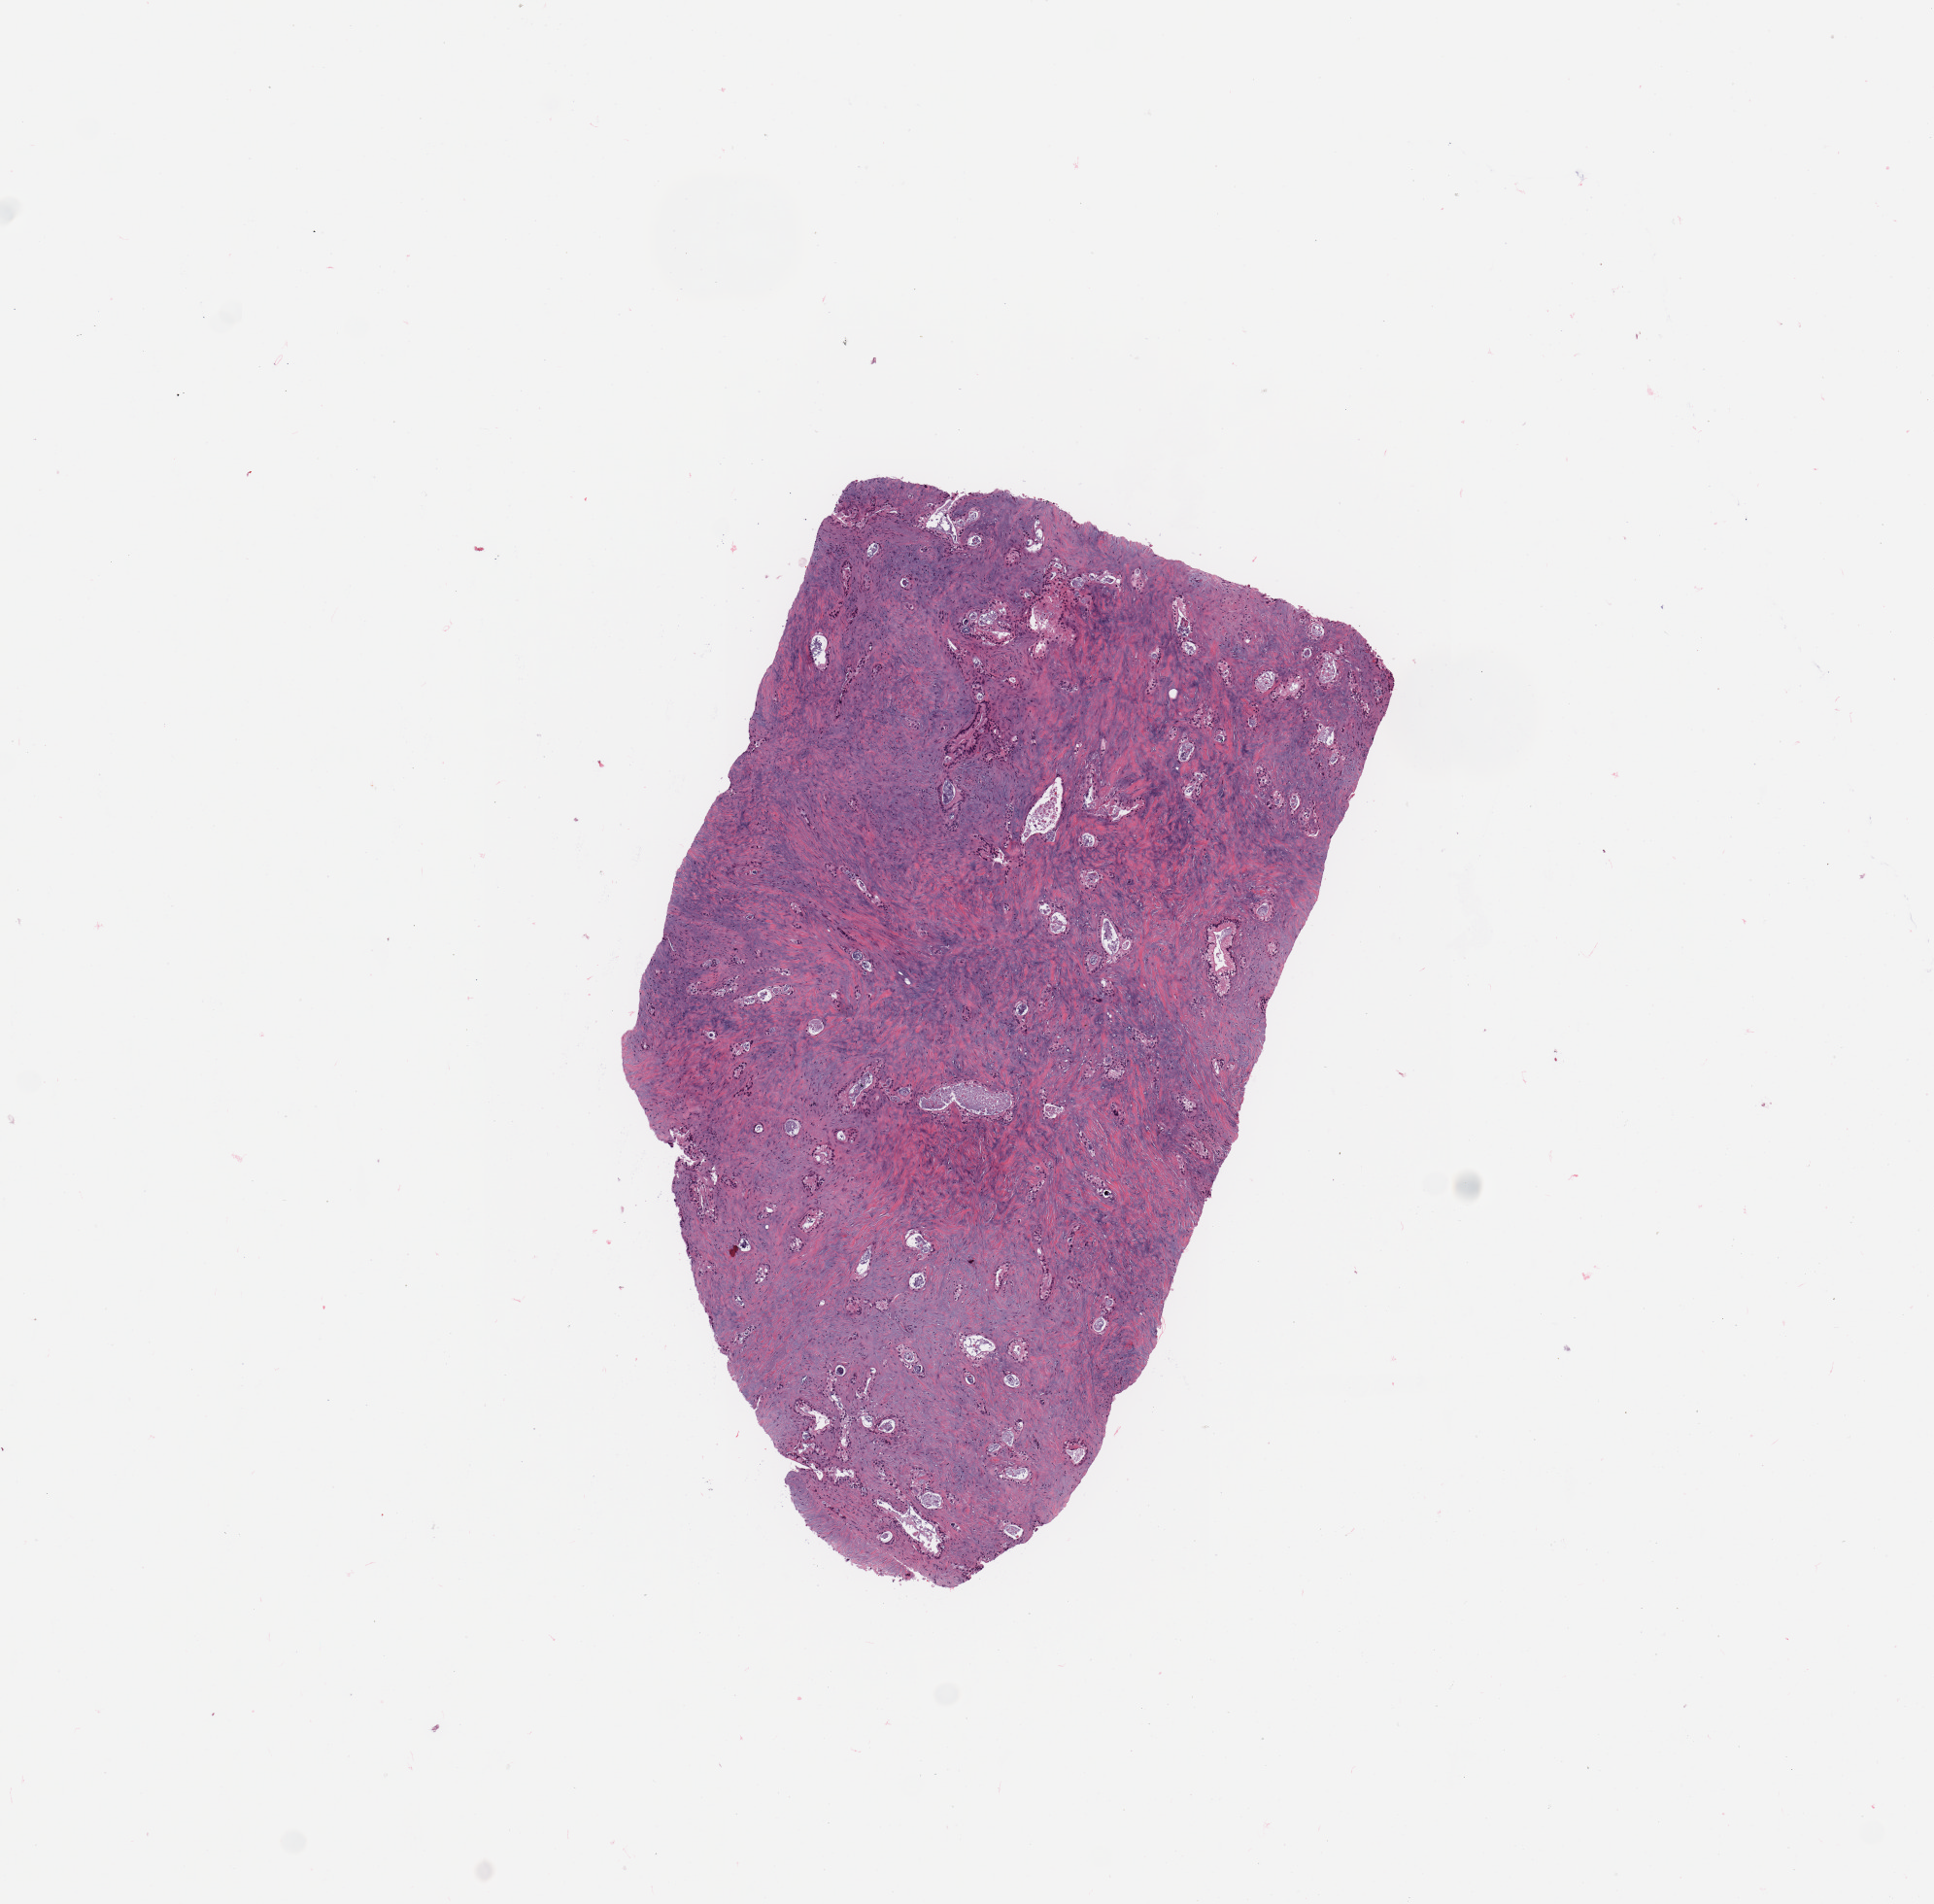
Digitized H&E-stained tissue section (whole slide) — low-resolution overview of the scanned area, about 7.9 x 7.8 mm (from a 20x scan); pancreas, tumour tissue. 84-year-old male patient. Histologic grade: G2 (moderately differentiated).
Diagnosis: Infiltrating duct carcinoma, NOS. AJCC pathologic stage: III. Primary tumour site (as recorded): head.